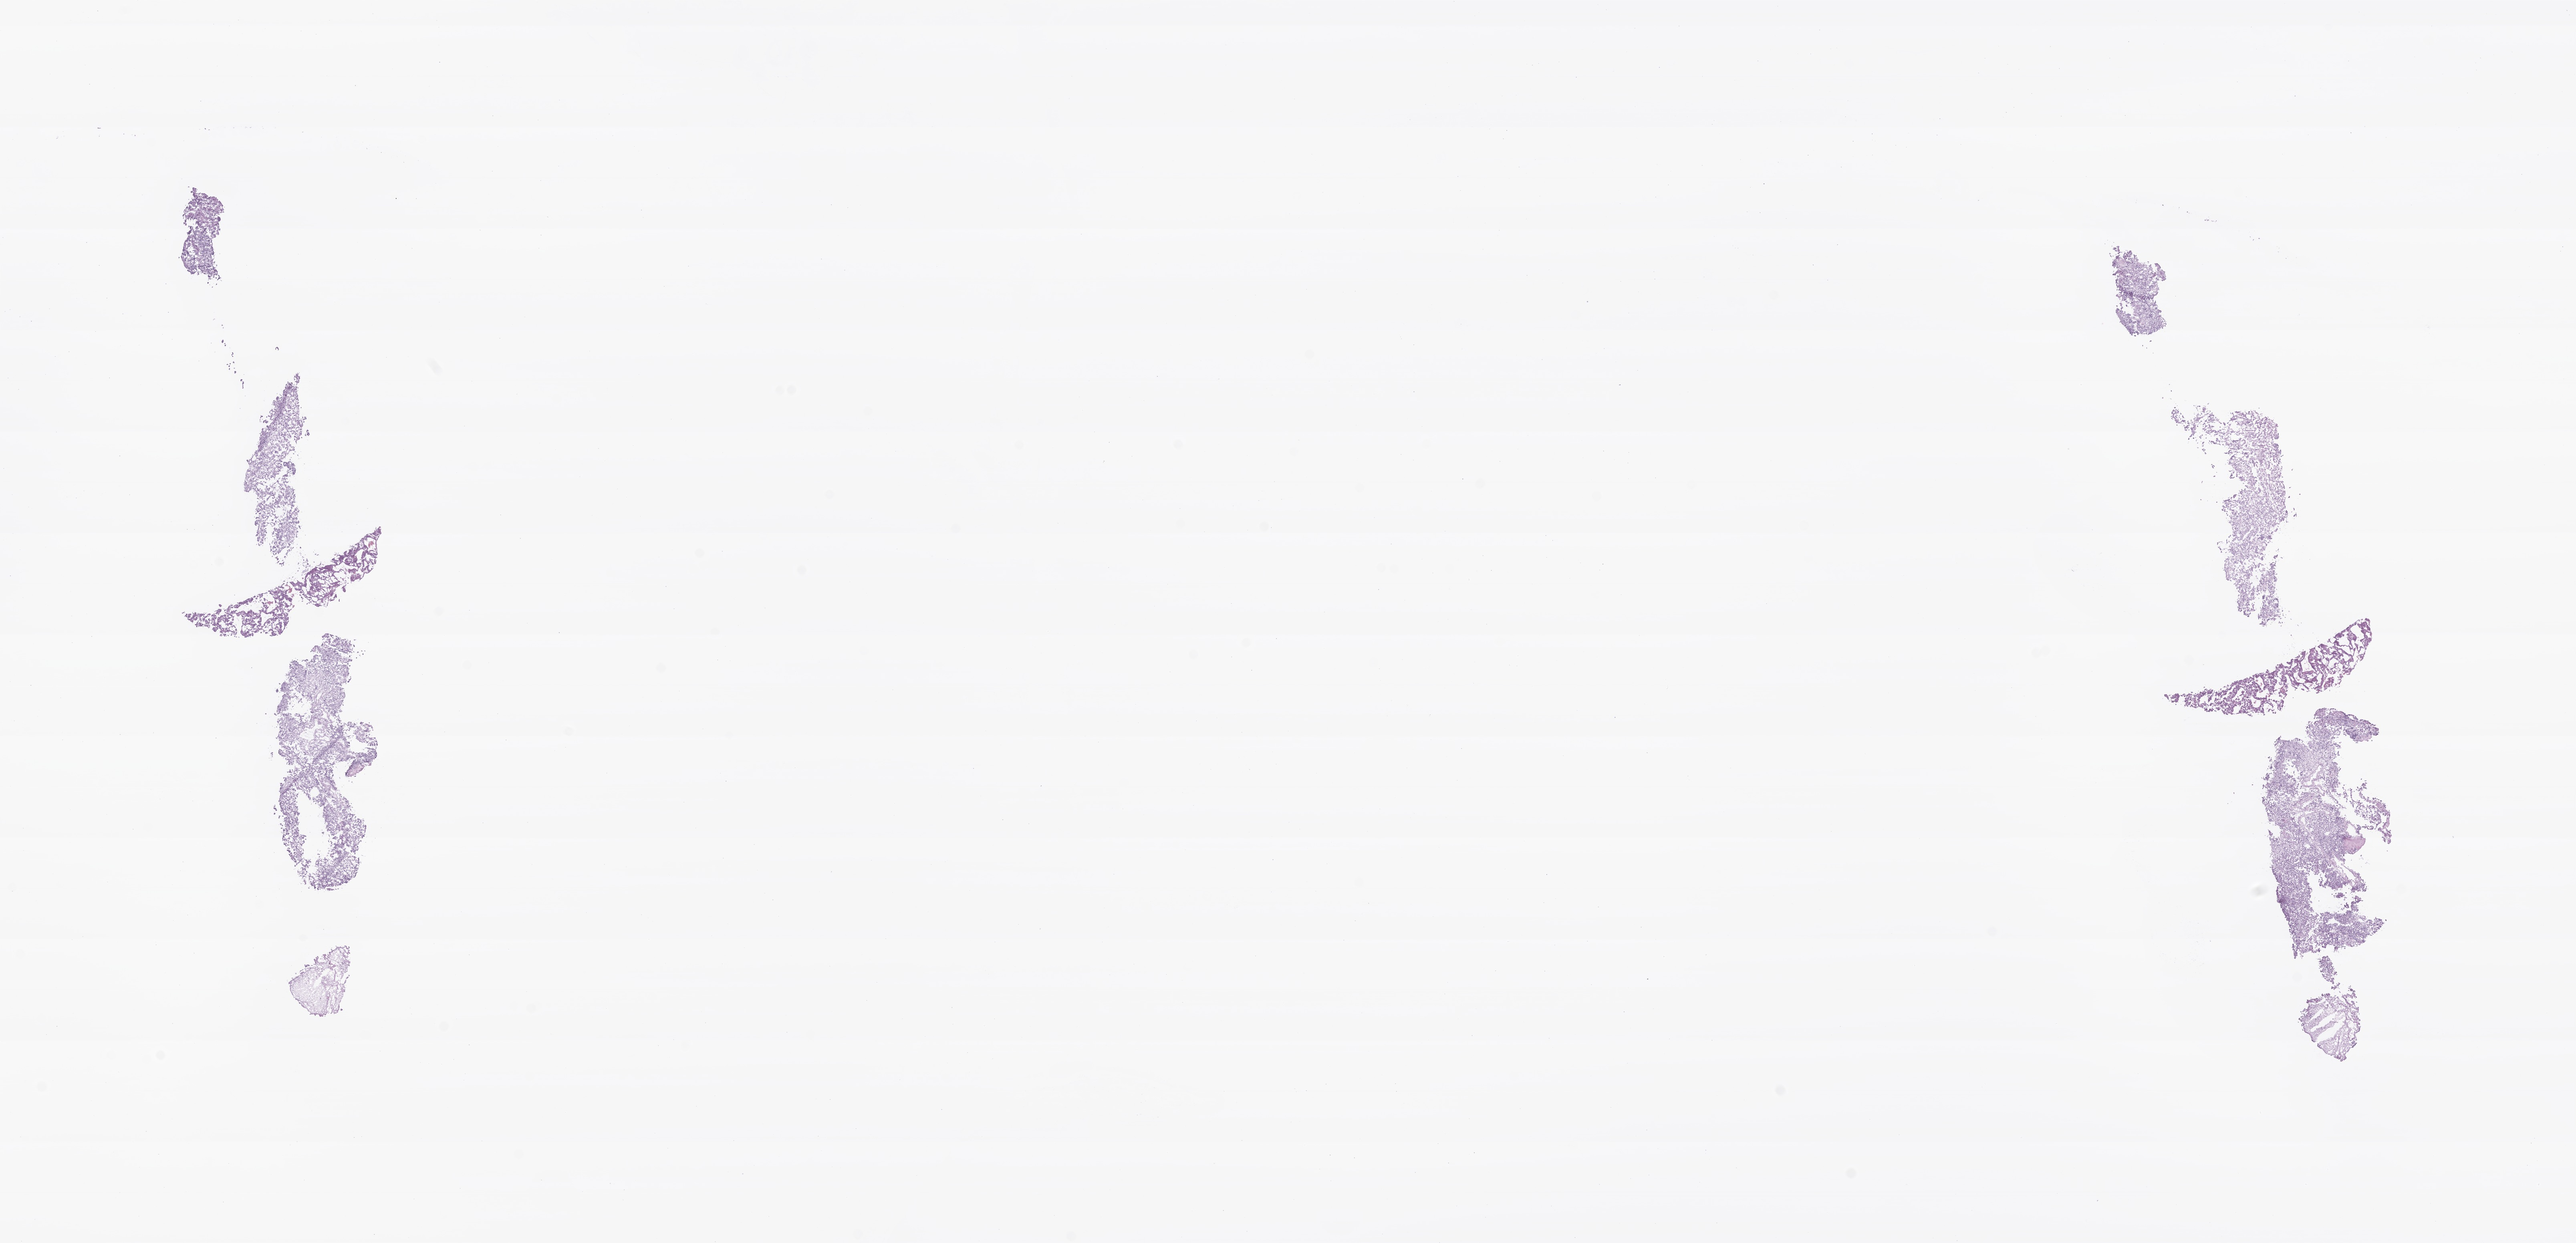
Digitized hematoxylin and eosin (H&E)-stained section of tumor tissue from the brain — low-resolution overview of the scanned area, about 27.0 x 13.0 mm. Frozen section. Female patient, age 115 months (9 years 7 months).
• diagnosis: Dysgerminoma